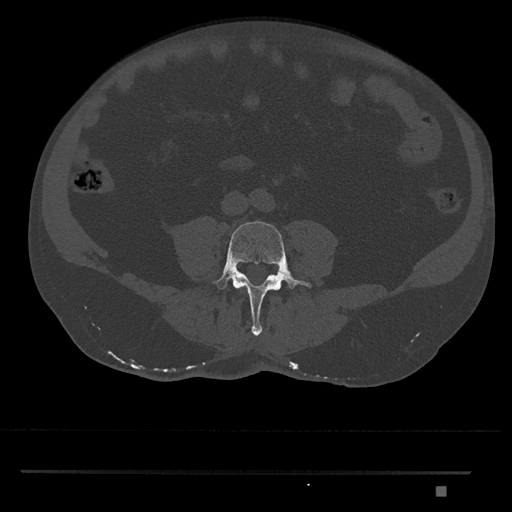
CT including the spine, one axial slice; position 616 of 1134 along the scan axis; reconstruction kernel Br40s/3; bone window (W 1800 / L 400 HU); 512 × 512 image matrix, field of view 429 × 429 mm. Patient: male, 65 years. Case-level facts recorded for this patient, not image findings: primary cancer: prostate.
Structures marked on this image (semi-automatically segmented with operator editing):
- L4 vertebra: bounding box (x1, y1, x2, y2) in pixels: (212, 221, 312, 336)